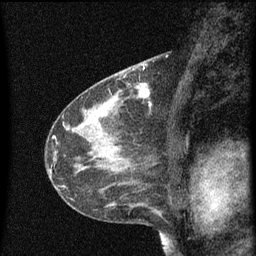
Breast MRI (dynamic contrast-enhanced), one sagittal slice. Slice 31 of 60 in the series (ordered by position). Dynamic contrast-enhanced series, image 2 of 3 at this slice position (ordered by acquisition). 1.5 T. TE 4.2 ms, TR 8 ms. 256 × 256 image matrix, field of view 180 × 180 mm. Patient: female, 41 years.
Outlined on this slice (semi-automatically segmented with operator editing):
- analysis volume of interest (the breast-tissue region the enhancement analysis was run in; not a lesion): box from (x=130, y=76) to (x=151, y=103) px
- tumour enhancement mask (voxels above the 70 % enhancement threshold inside the analysis volume of interest): (x=134, y=84)–(x=151, y=103)